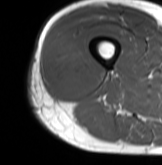
MRI of an extremity soft-tissue mass, one axial slice. Position 27 of 61 along the scan axis. MR volume resampled by the dataset authors to the PET/CT grid (not the native acquisition matrix). 3.27 mm slice thickness. 162 × 165 image matrix, field of view 158 × 161 mm. Male patient. Case-level facts recorded for this patient, not image findings: histological type: poorly differentiated synovial sarcoma; grade: high; site of the primary tumour: right buttock.
Structures marked on this image (expert contour drawn on MRI and transferred to this co-registered scan by the dataset authors):
- gross tumour volume including surrounding oedema: bounding box [x1, y1, x2, y2] px = [48, 33, 94, 96]
- gross tumour volume (mass): [50, 42, 92, 96]